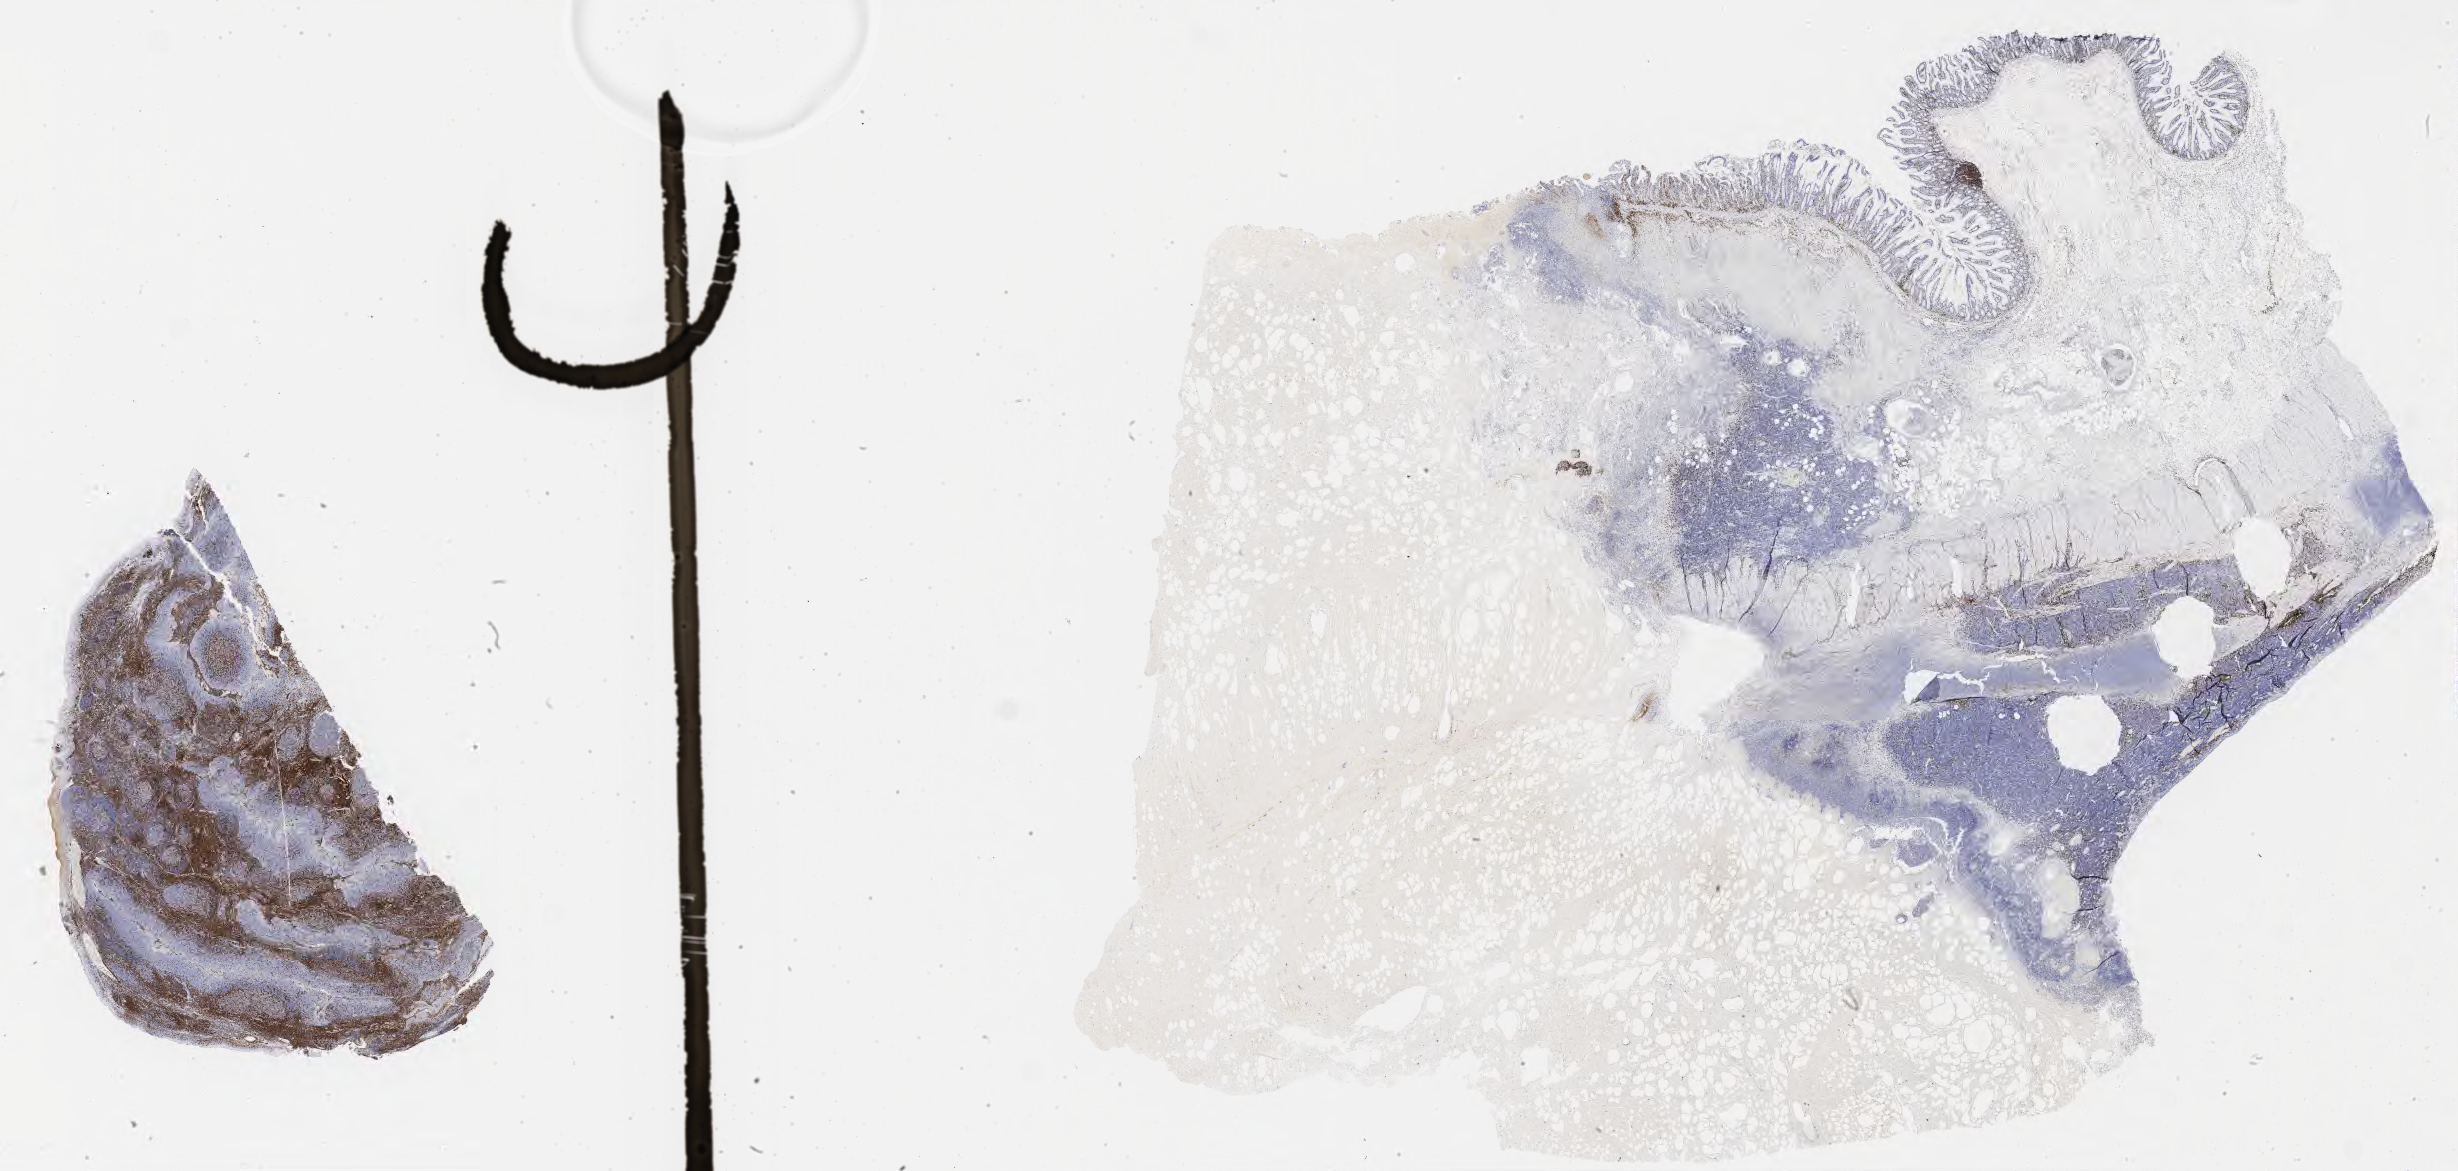
IHC for CD3, whole-slide image — low-resolution overview of the scanned area, about 39.8 x 18.9 mm; tumor tissue; anatomic site: colon. Male patient, 62 years old.
Histologic diagnosis: Burkitt lymphoma, NOS.